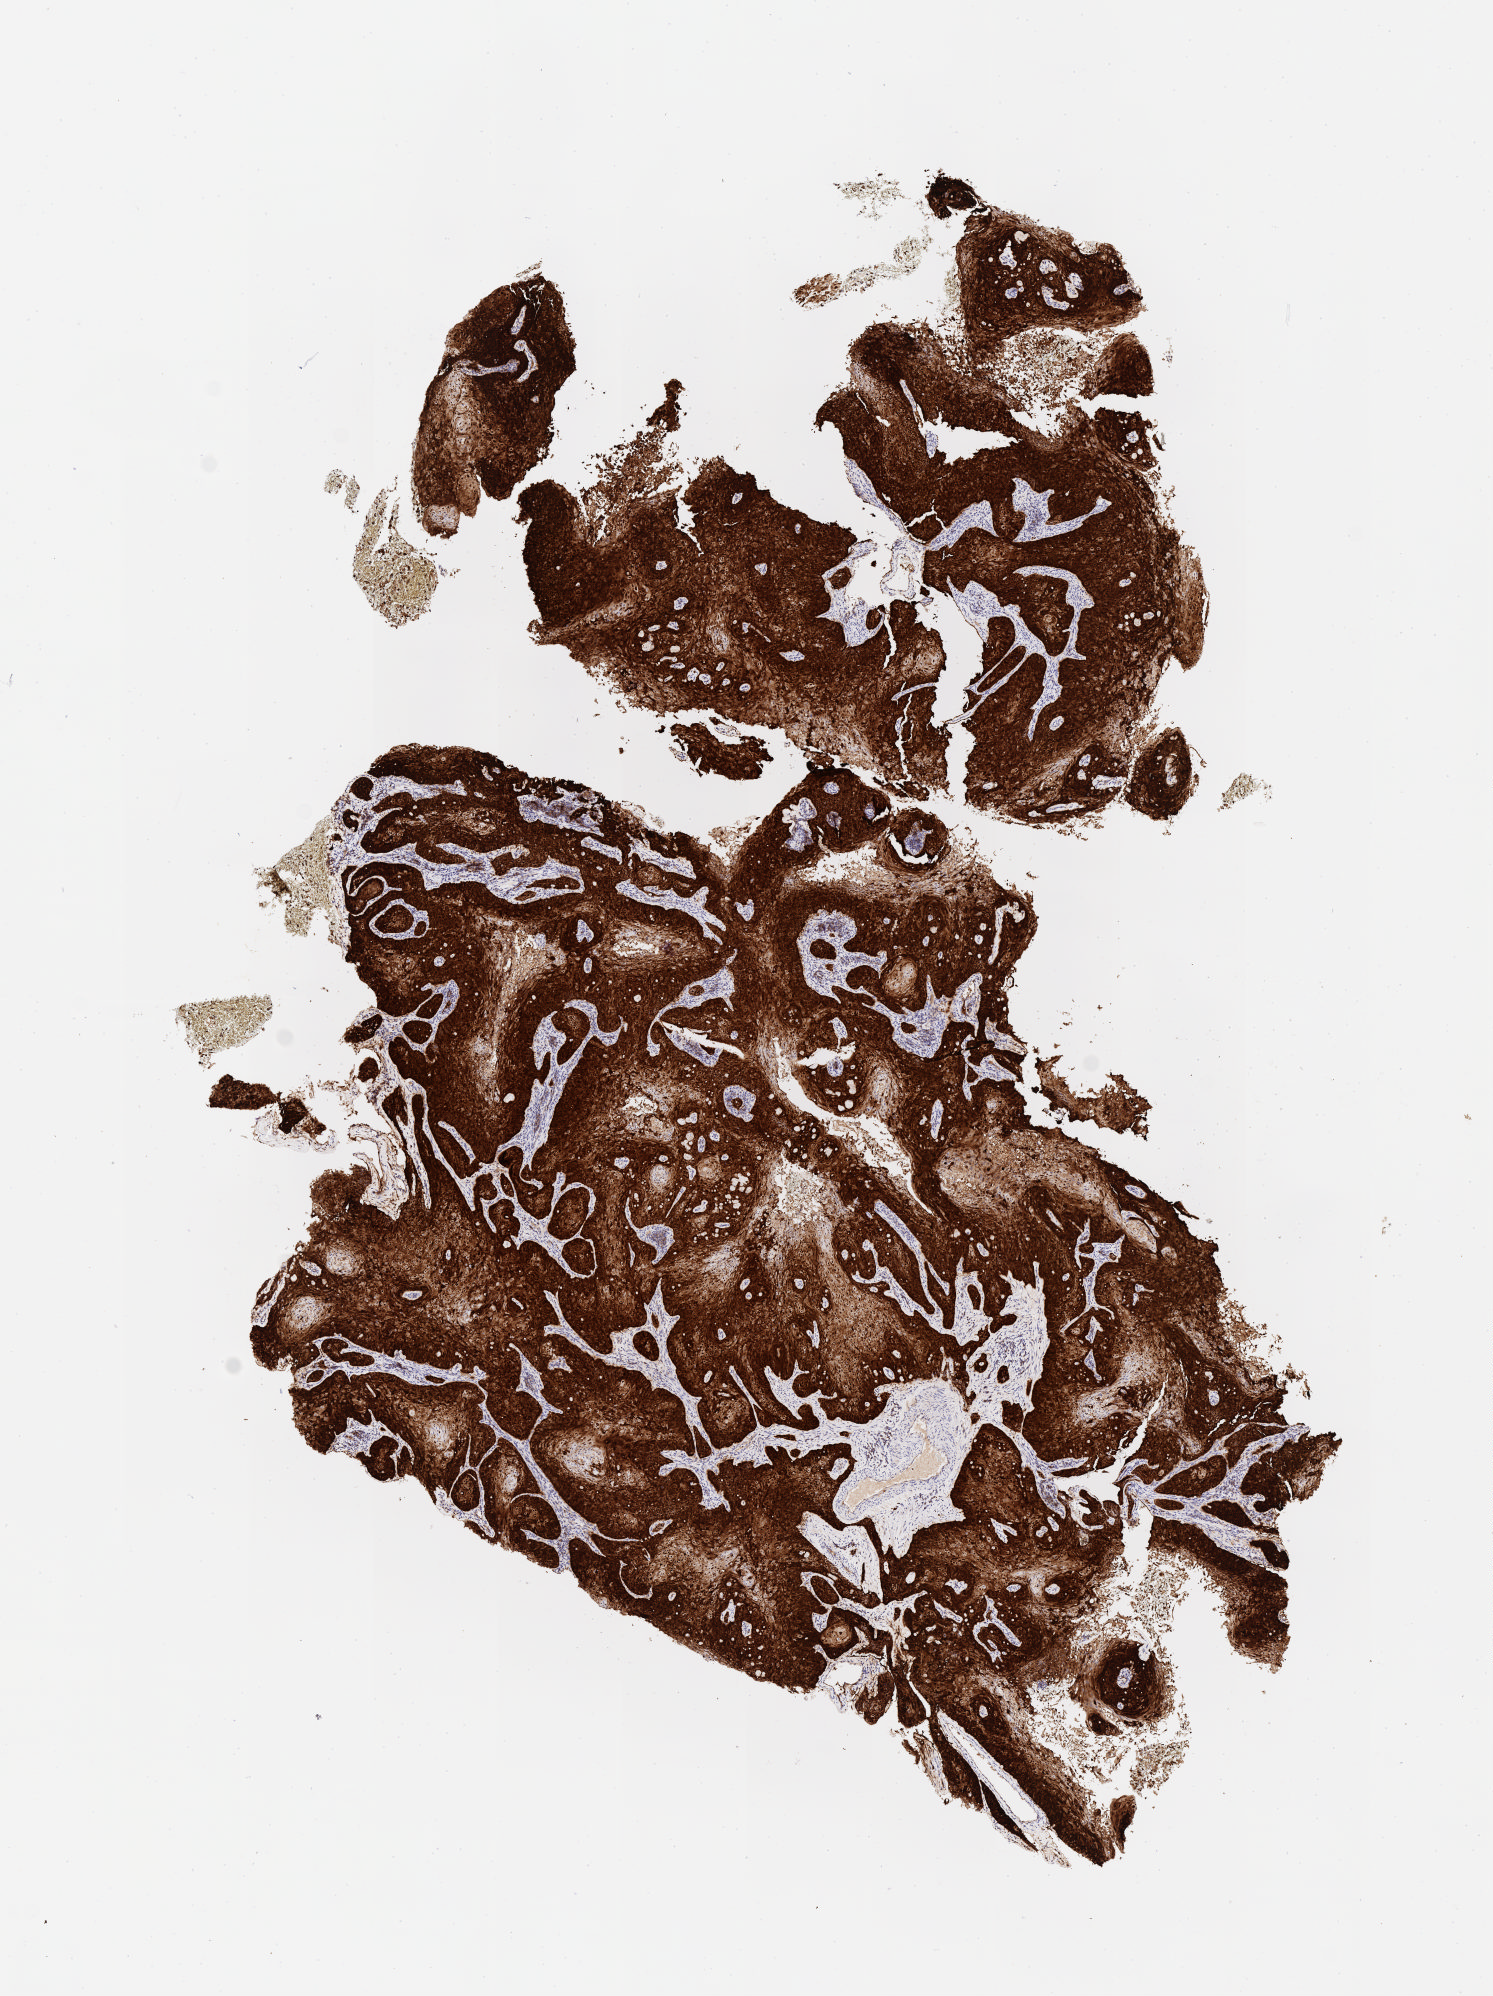
IHC for p16 (p16INK4a), whole-slide image, low-resolution overview of the scanned area, about 6.0 x 8.1 mm, specimen: tumor tissue, anatomic site: cervix. Patient: female, 46 years old.
- histologic diagnosis: Squamous cell carcinoma, keratinizing, NOS